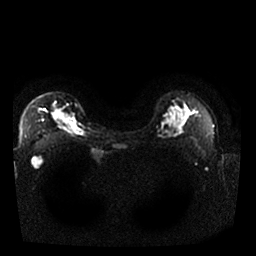
Breast MRI, one axial slice; position 20 of 25 along the scan axis; diffusion-weighted series; image 2 of 4 stored at this slice position (different b-values; order by instance number); 1.5 T; 4 mm slice thickness; 256 × 256 image matrix. Female patient.
Outlined on this slice (manually delineated by an expert):
- tumour on diffusion-weighted imaging: box from (x=54, y=110) to (x=65, y=120) px